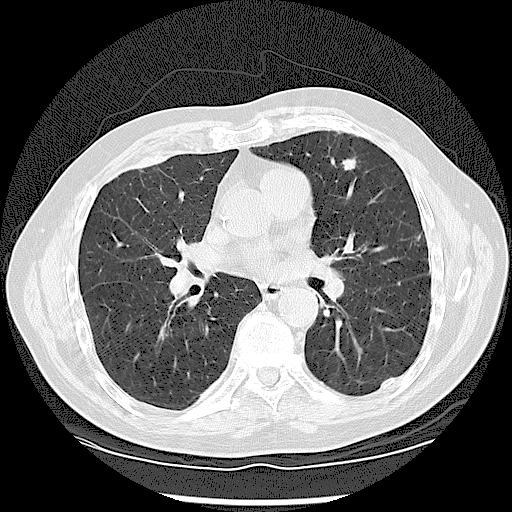
Low-dose screening chest CT, one axial slice. Position 56 of 120 along the scan axis. Reconstruction kernel LUNG. Lung window (W 1500 / L -600 HU). 512 × 512 image matrix.
Outlined on this slice (expert manual segmentation):
- lesion 1 (tumor, upper lobe of left lung): bounding box (x1, y1, x2, y2) in pixels: (342, 159, 356, 170)